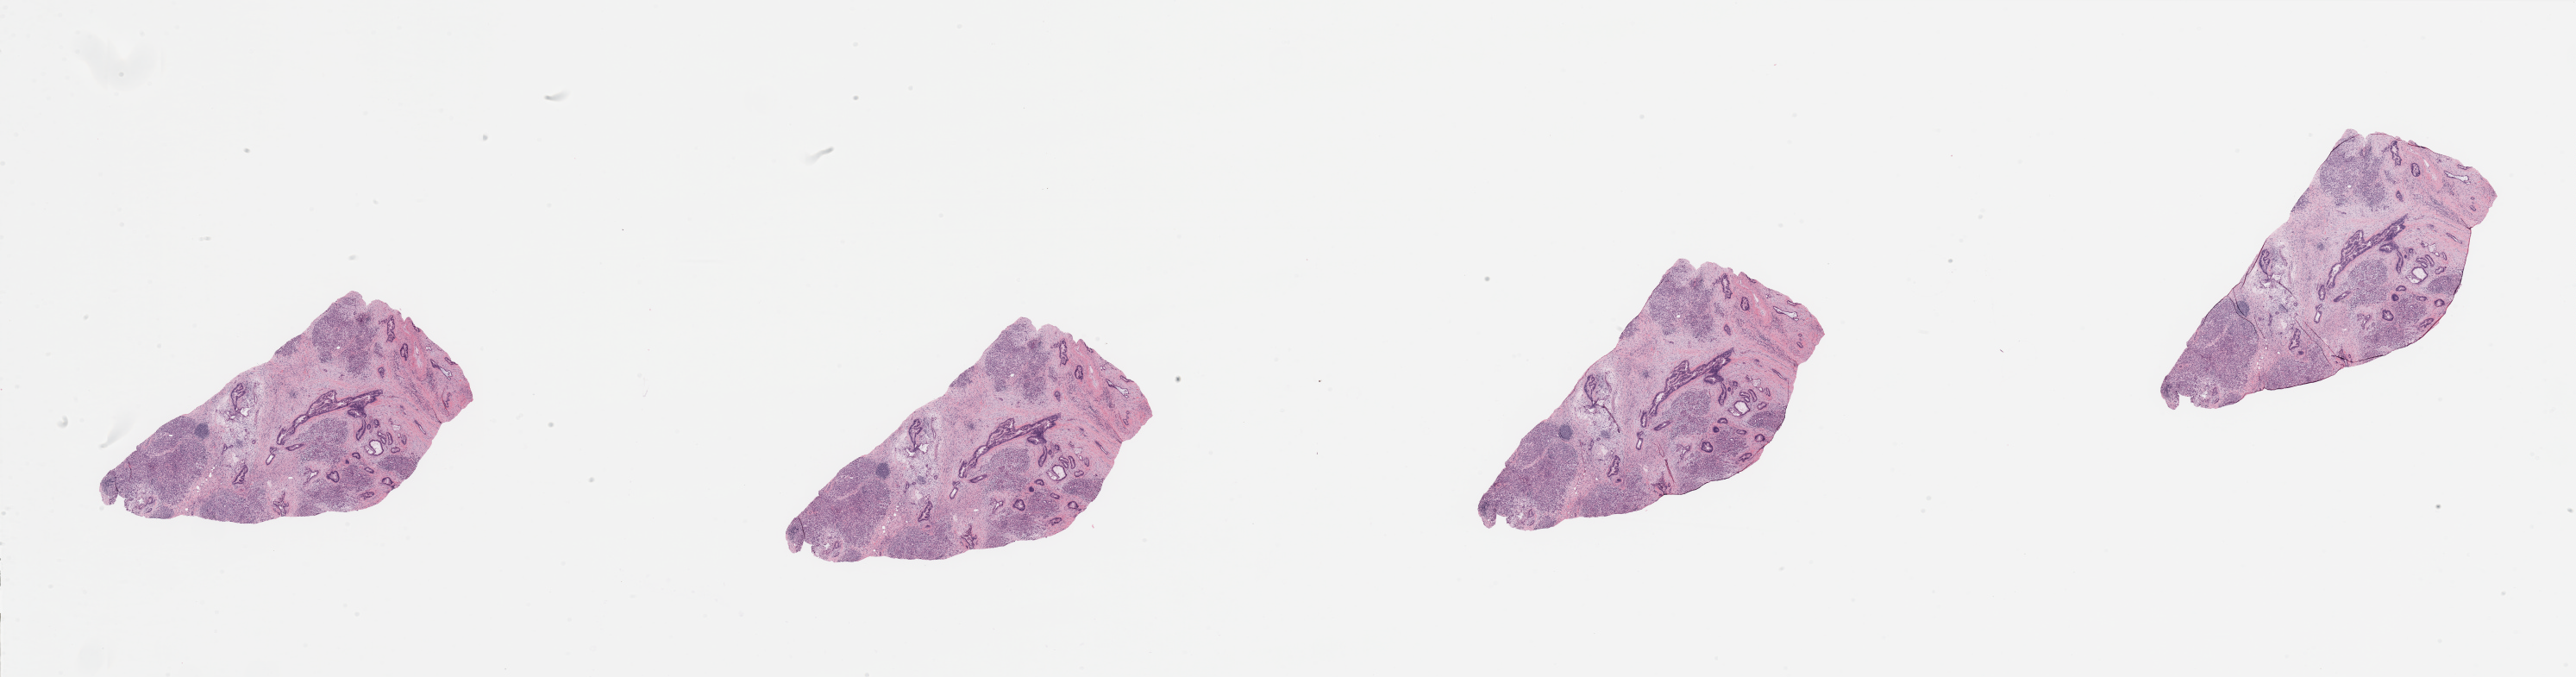
Whole-slide histology image, Hematoxylin and eosin (H&E) stained, whole scanned area (about 47.3 x 12.4 mm) shown as a low-resolution overview, tumour tissue sample, sampled site: pancreas. 78-year-old female patient. Histologic grade: G2 (moderately differentiated). Composition of this section per pathologist review: tumour nuclei 15%, necrosis 0%.
* histologic diagnosis: Infiltrating duct carcinoma, NOS
* primary tumour site (as recorded): head
* AJCC pathologic stage: IIB